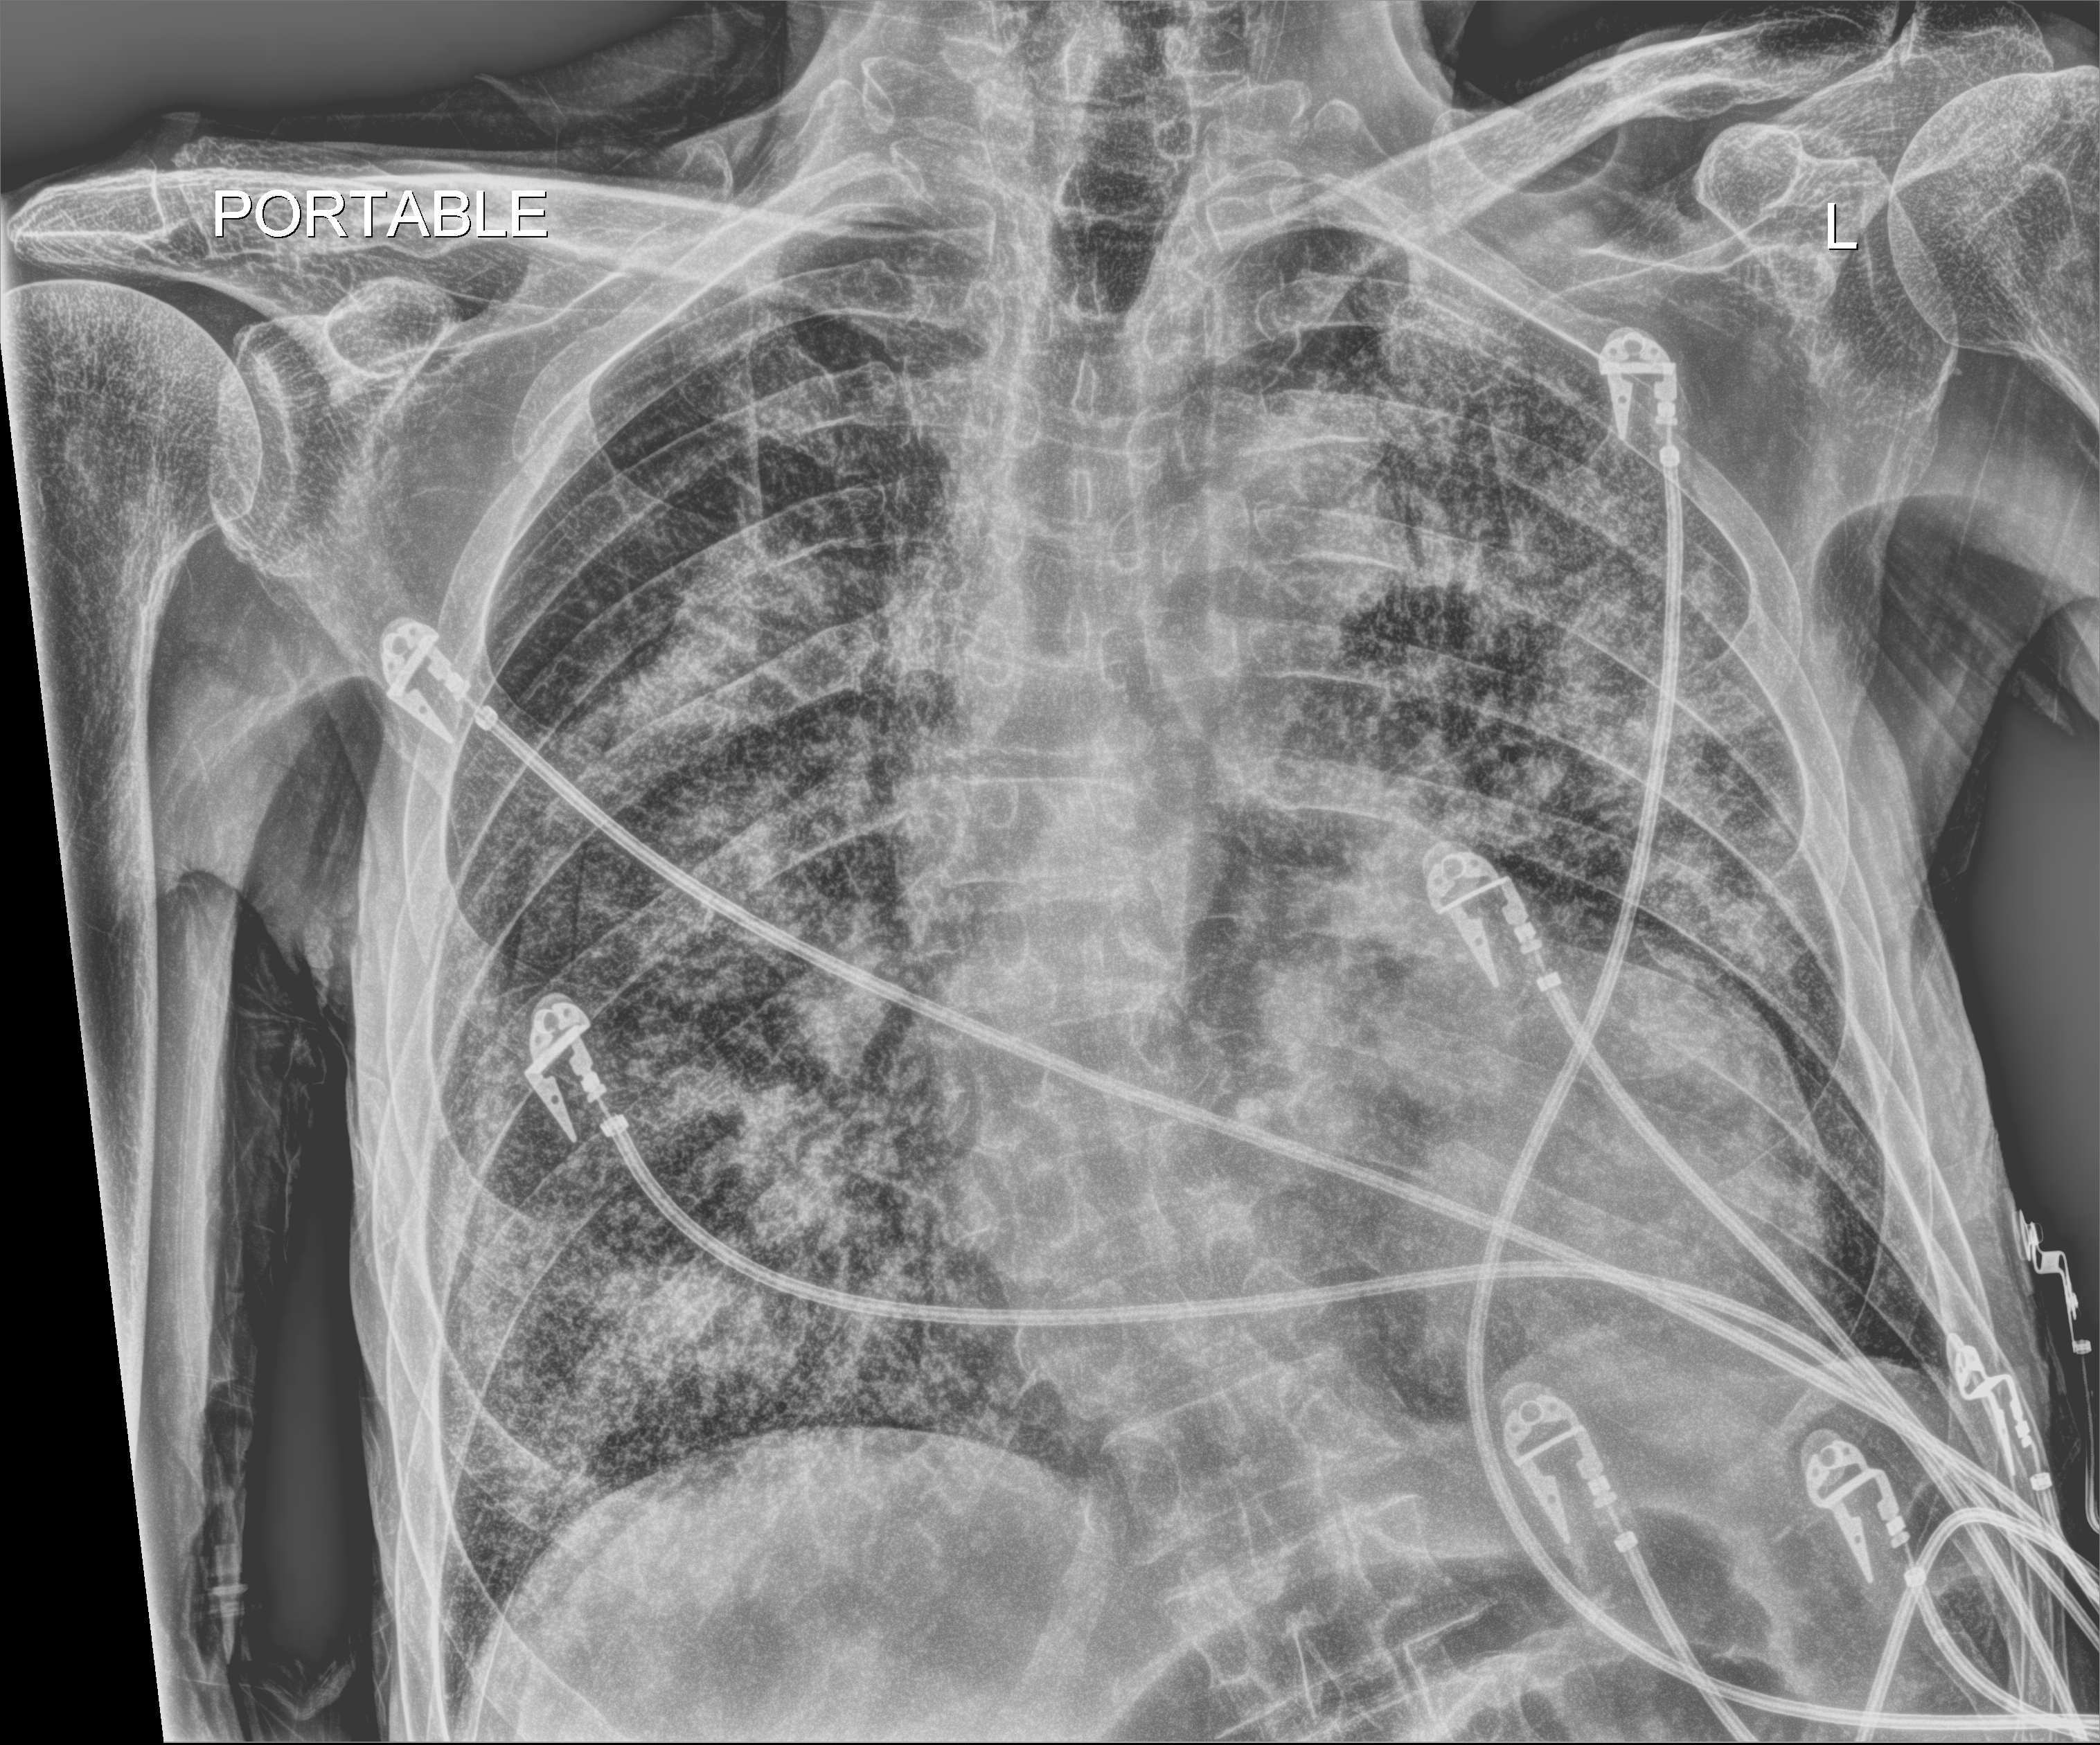
Chest radiograph. Male patient hospitalised with COVID-19, age 75–90 years.
Admission-level facts for this patient (not findings on this image; timing relative to this image not recorded): mechanically ventilated during this hospital stay: no; admitted to intensive care during this hospital stay: no.